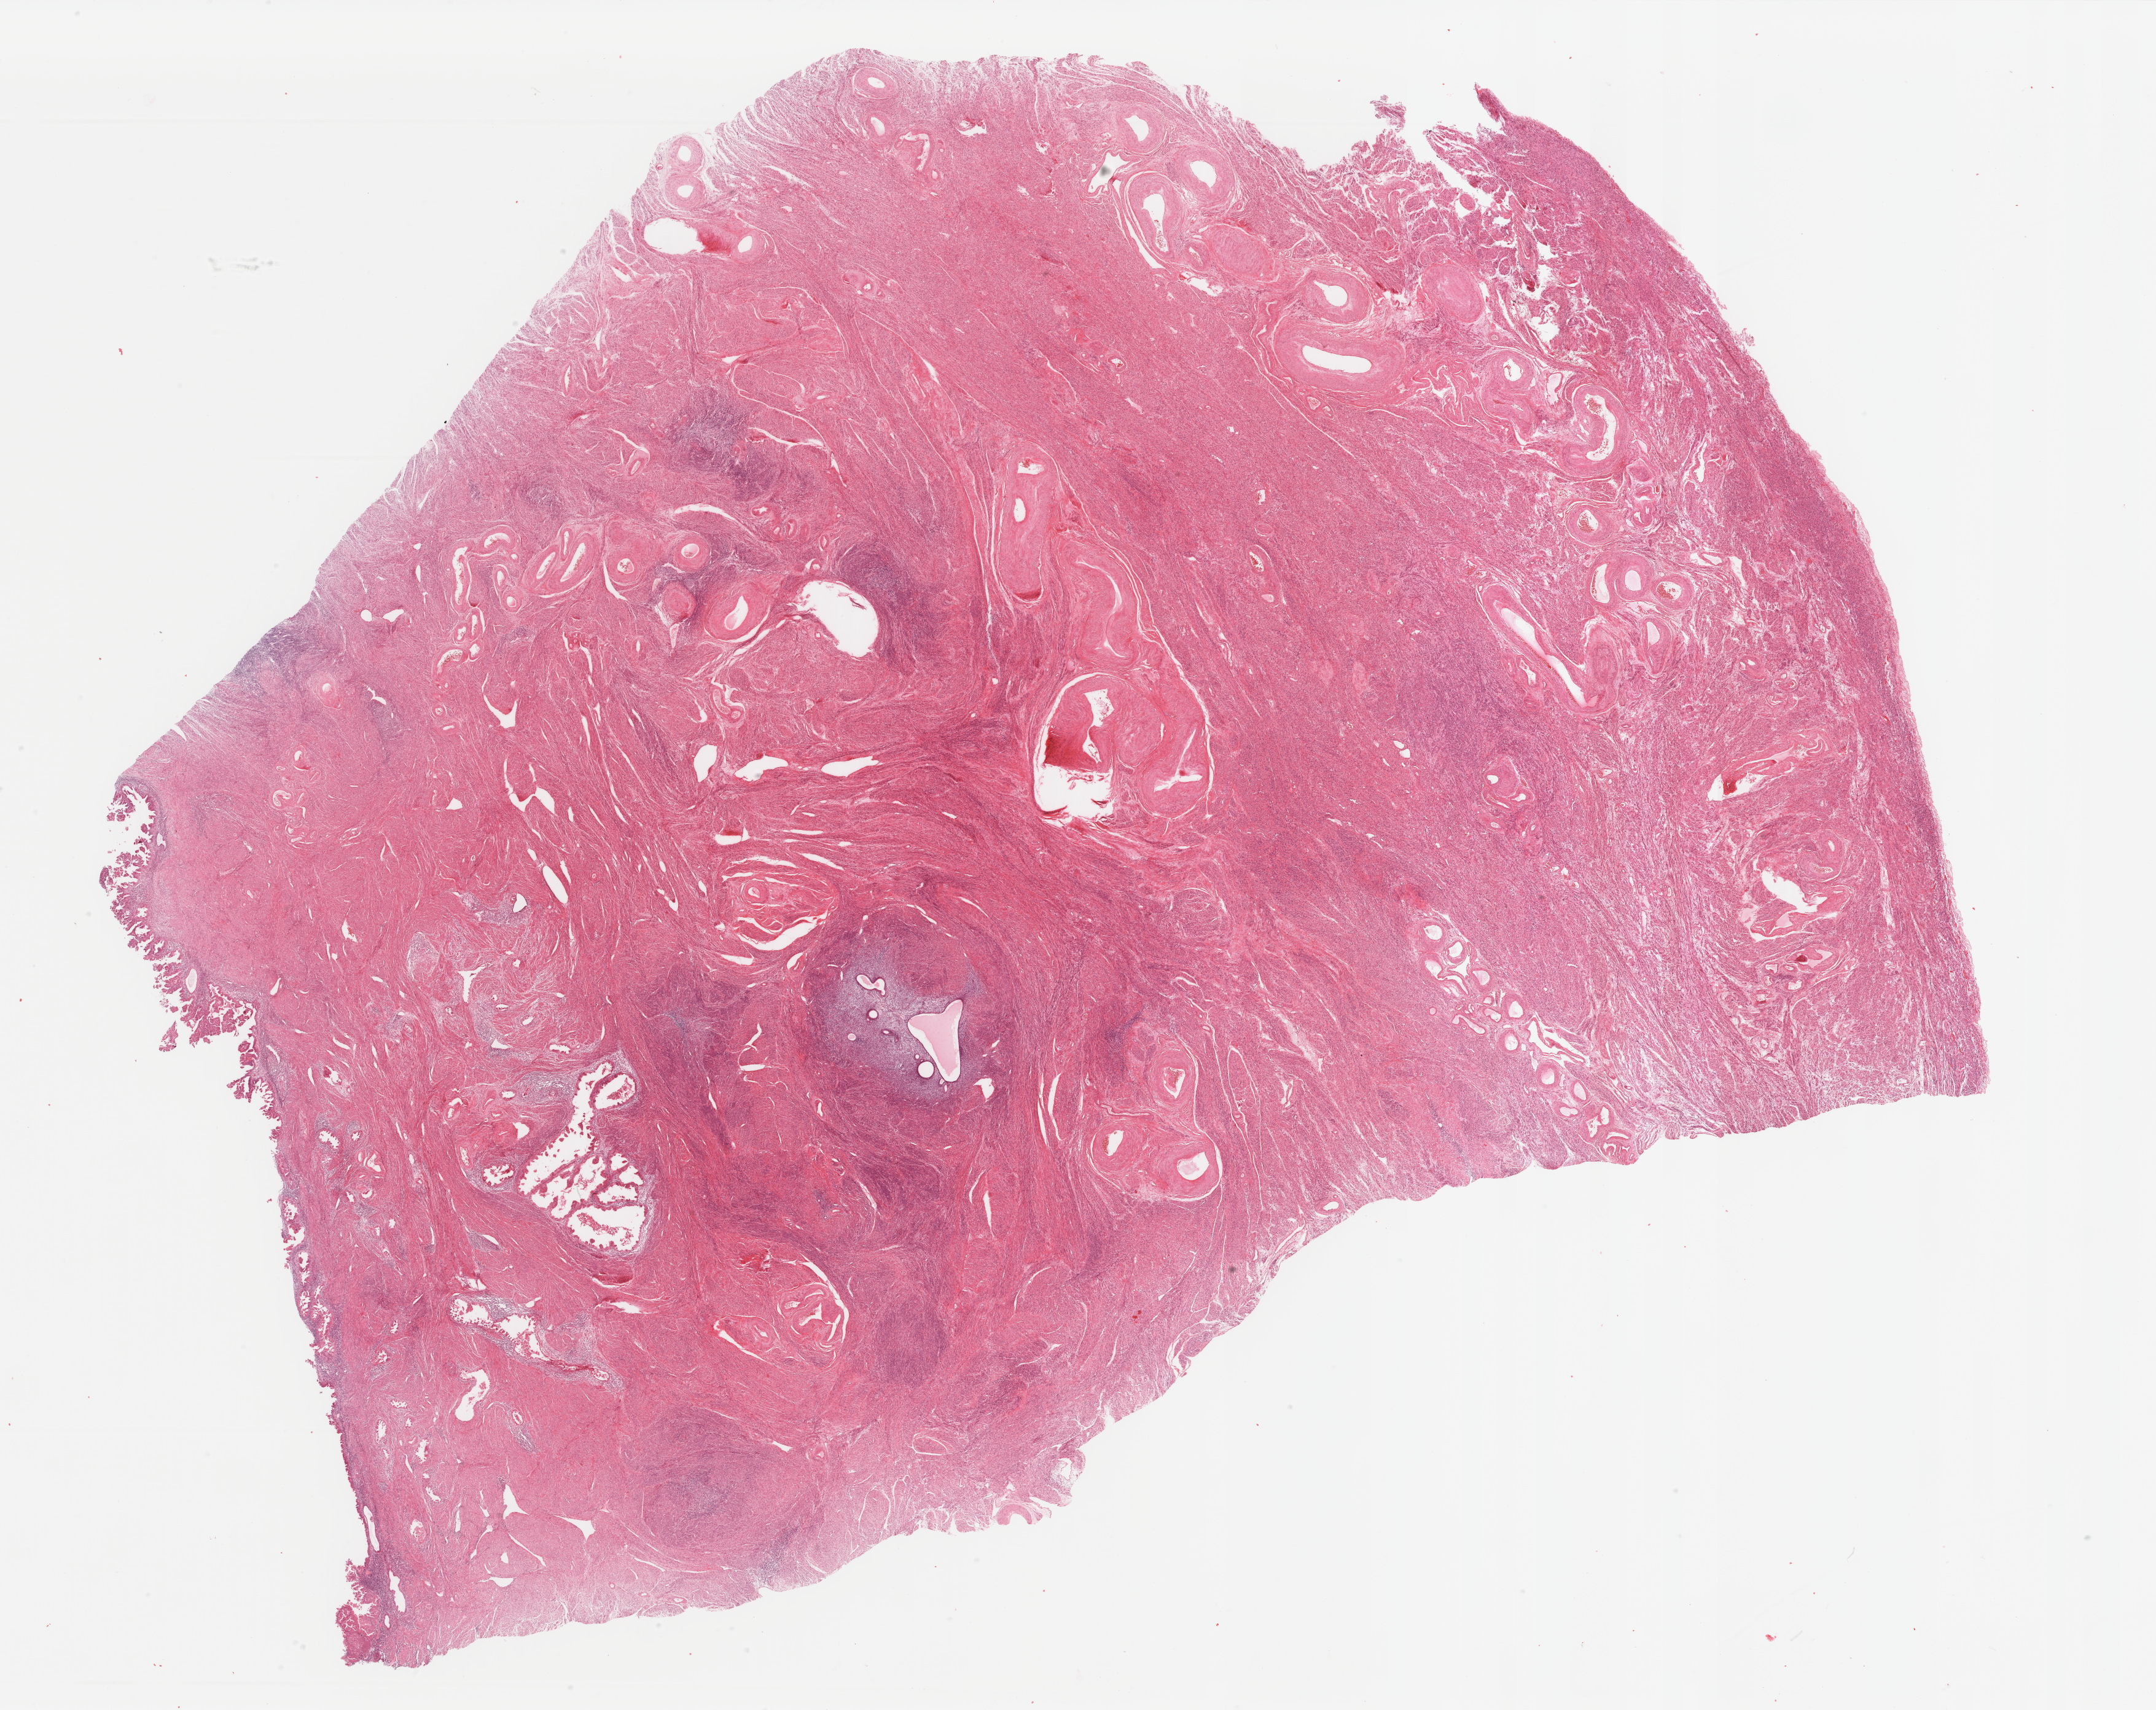
H&E-stained whole-slide image, low-resolution overview of the scanned area, about 27.9 x 22.1 mm; FFPE section; primary tumour sample from the uterus. Female, age 70 years at initial diagnosis. Histologic grade: G3 (poorly differentiated).
FIGO stage: IB. Diagnosis: Serous cystadenocarcinoma, NOS (endometrium). Lymph nodes positive (case pathology): 0 of 10 examined.